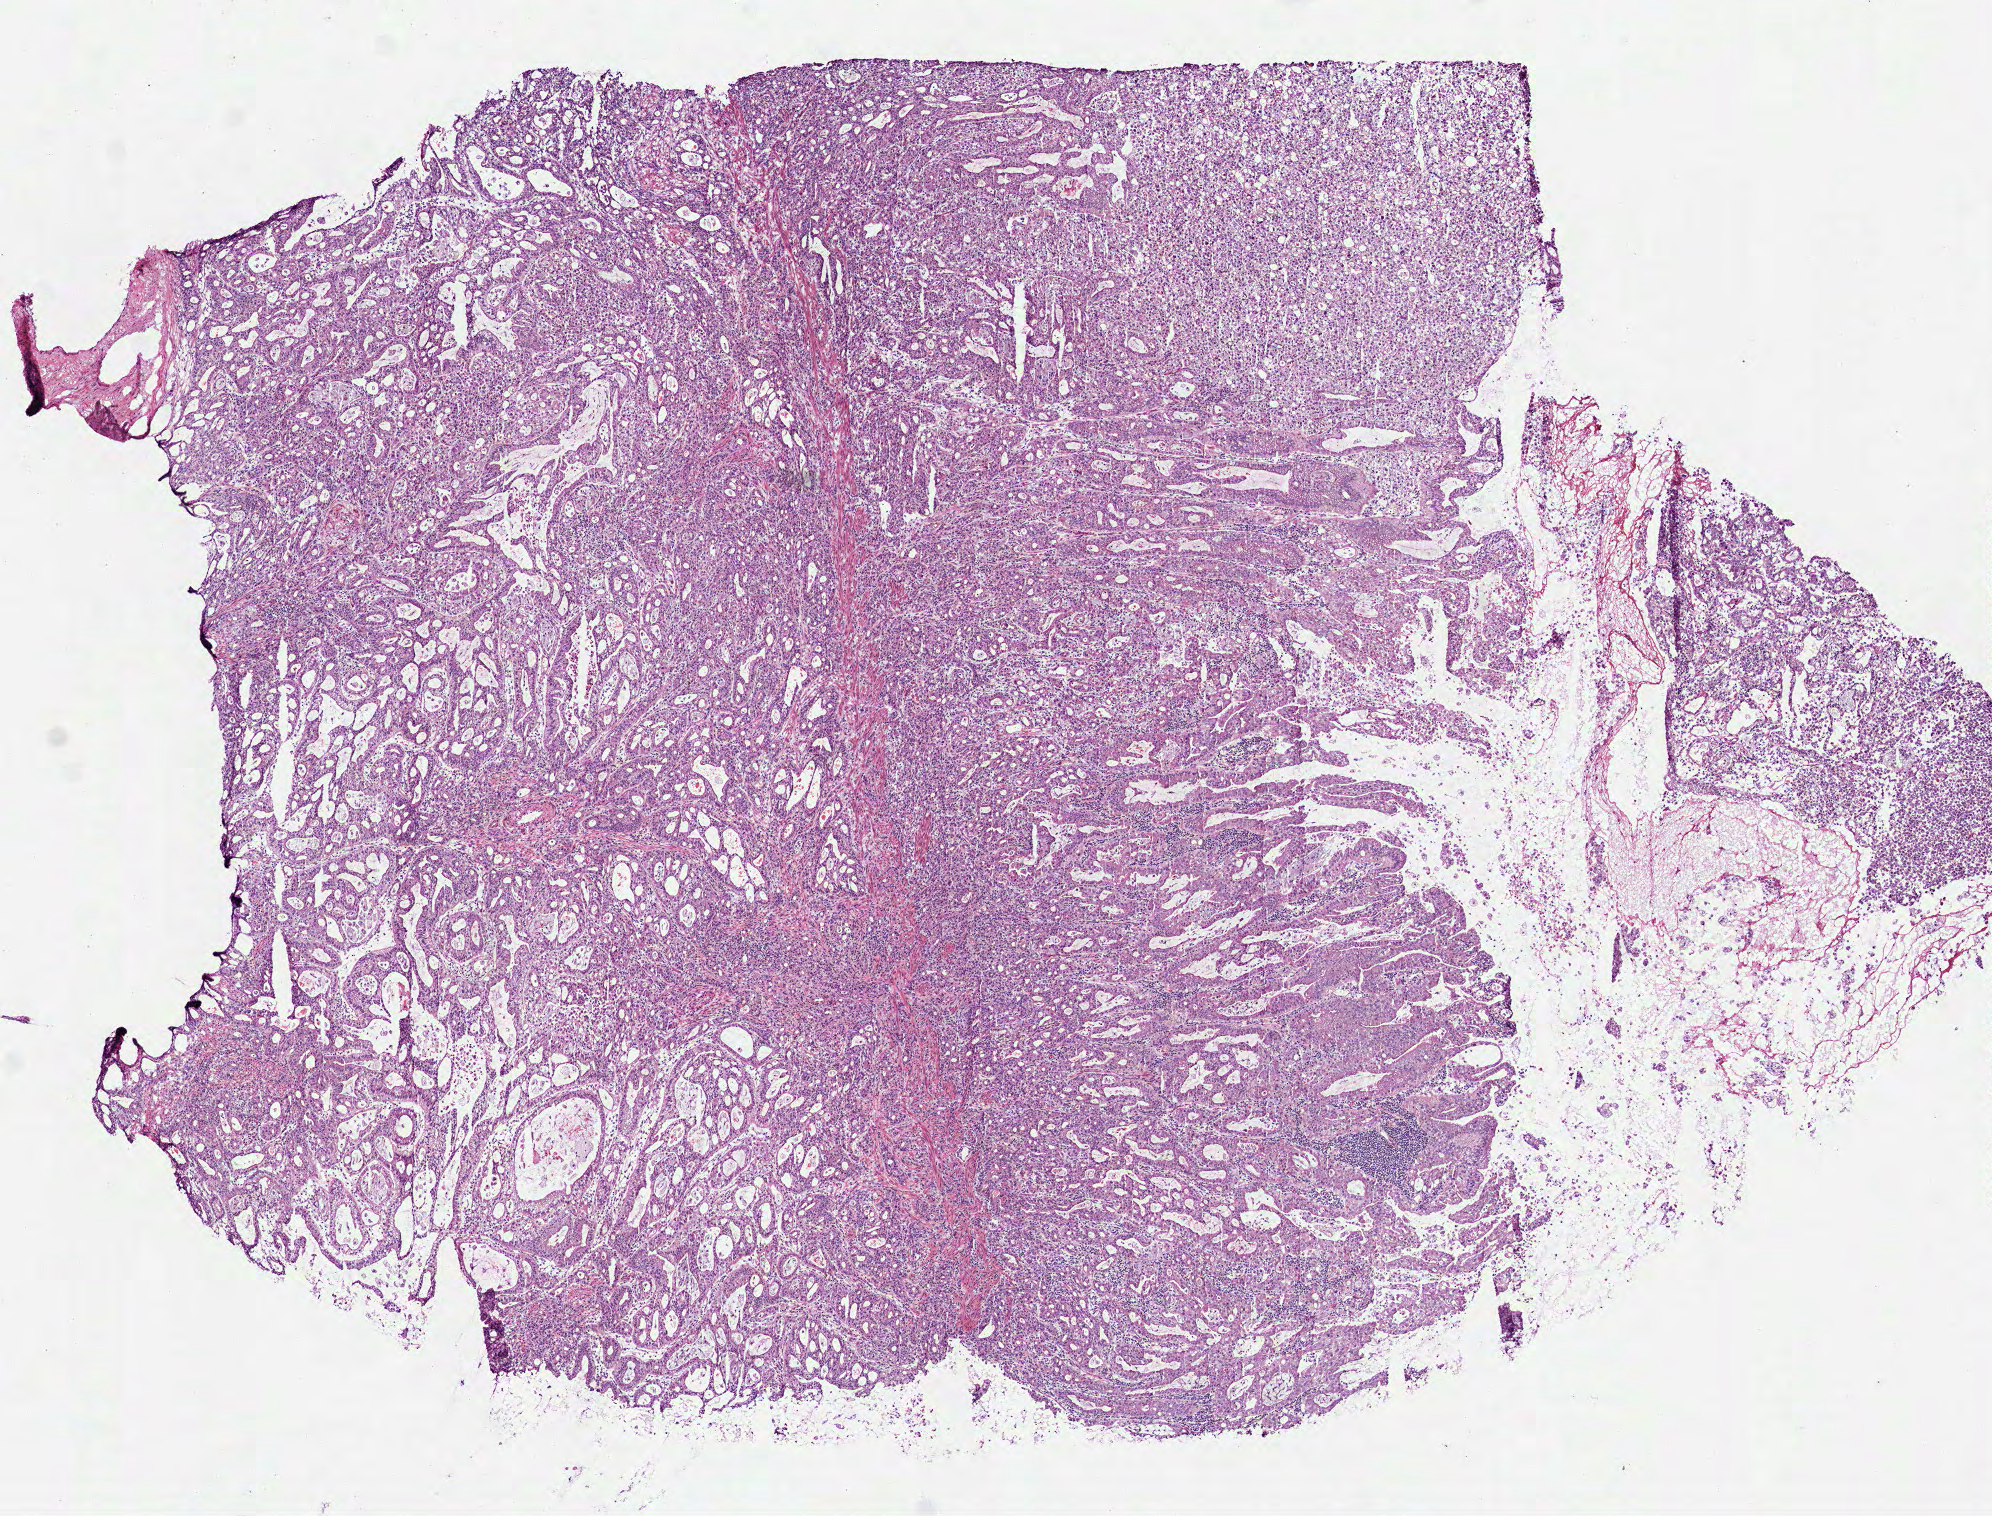
H&E-stained whole-slide image — whole scanned area (about 8.0 x 6.1 mm) shown as a low-resolution overview; frozen section from the bottom of the tissue portion; primary tumour sample from the stomach. Male patient; age at initial diagnosis 75 years. Histologic grade: G3 (poorly differentiated). Pathologist review of this section (percent, as recorded): tumour cells 99%, tumour nuclei 85%, normal cells 0%, stromal cells 0%, necrosis 1%. Inflammatory infiltration, as recorded: lymphocyte infiltration 10%, monocyte infiltration 0%, neutrophil infiltration 5%.
* AJCC pathologic stage: IIIA (7th edition)
* diagnosis: Tubular adenocarcinoma
* lymph nodes positive (case pathology): 6 of 15 examined